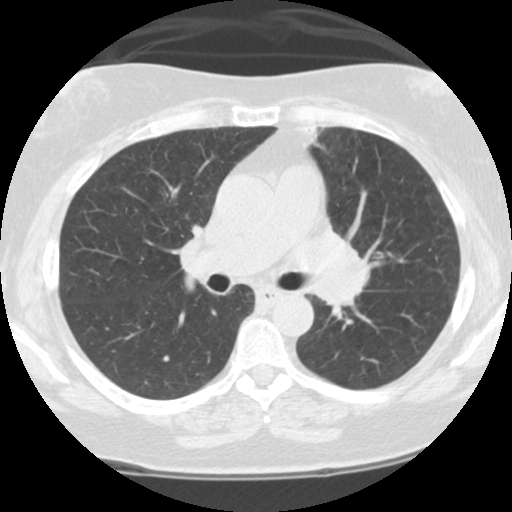
Axial slice from a low-dose chest CT screening exam, third screening round (two years after baseline), lung window (W 1500 / L -600 HU), standard (soft-tissue) reconstruction kernel (STANDARD), slice 44 of 108 in the series. Female, age 59 years at enrolment. Current smoker at enrolment.
• Expert reader's lesion annotation, bounding box (x1, y1, x2, y2) in pixels: (285, 213, 387, 325).
• No non-calcified nodule or mass ≥4 mm was recorded by the screening reader at this exam.
• Official screen result: positive, other.
• Participant outcome: lung cancer diagnosed 192 days after this screen — small cell carcinoma, NOS, left upper lobe, left hilum, mediastinum, left main stem bronchus, stage IV (AJCC 6th edition), 63 mm at pathology.